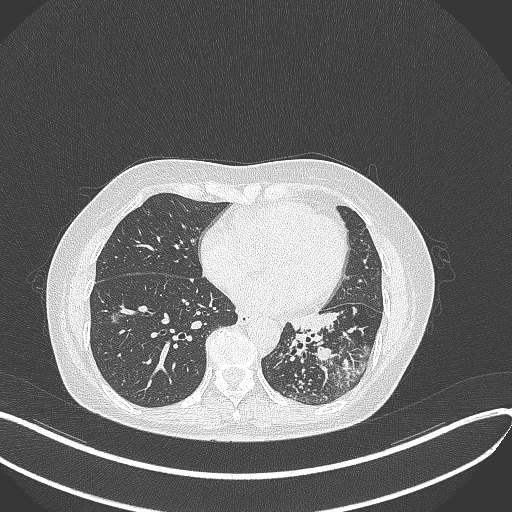
Chest CT, one axial slice. Position 155 of 429 along the scan axis. Reconstruction kernel B70f. Lung window (W 1500 / L -600 HU). 1 mm slice thickness. 512 × 512 image matrix, field of view 400 × 400 mm. Female patient, age 63 years. From the clinical record (not read from this slice): clinical TNM (as recorded): T1b N0 M0.
Structures marked on this image (bounding box drawn by a radiologist):
- lung tumour (recorded histology: adenocarcinoma): box from (x=286, y=305) to (x=339, y=343) px